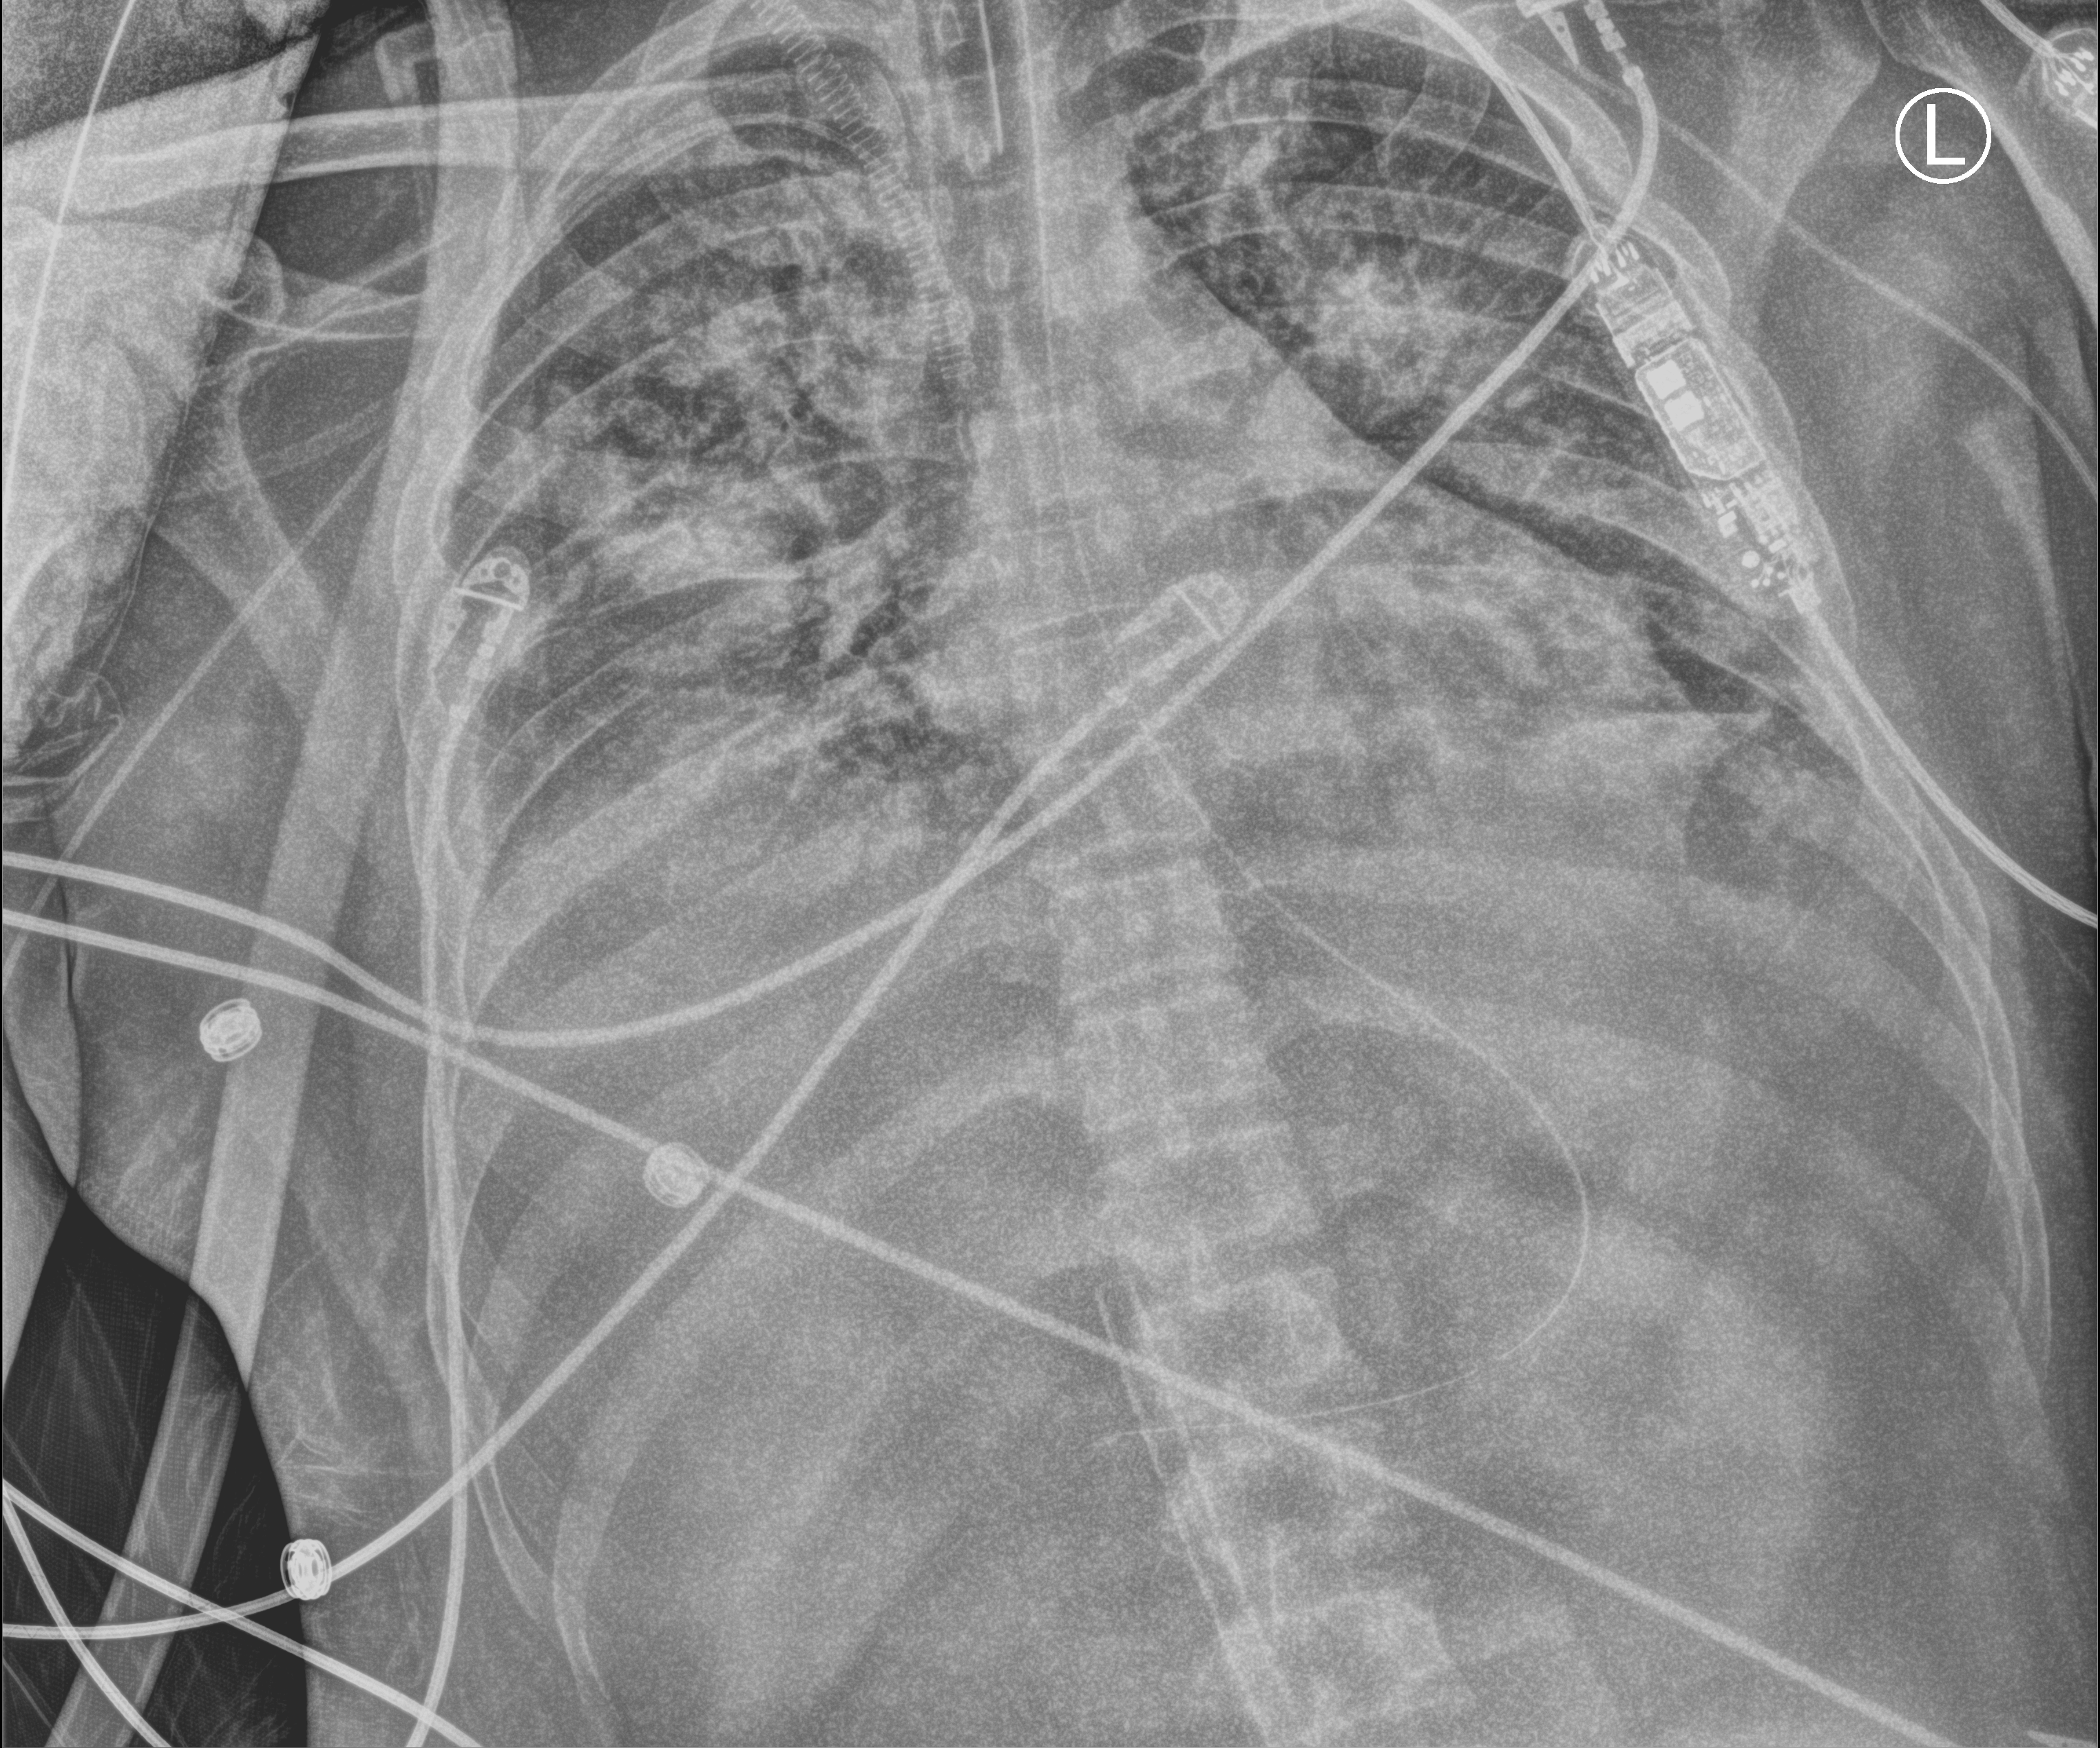
Bedside chest radiograph (computed radiography); anteroposterior (AP) projection. Patient hospitalised with COVID-19, aged 18–59 years.
From the hospital-stay record, not from the radiograph (when in the stay this image was taken is not recorded): admitted to intensive care during this hospital stay: yes; COPD (admission record): no; length of hospital stay: 60 days.